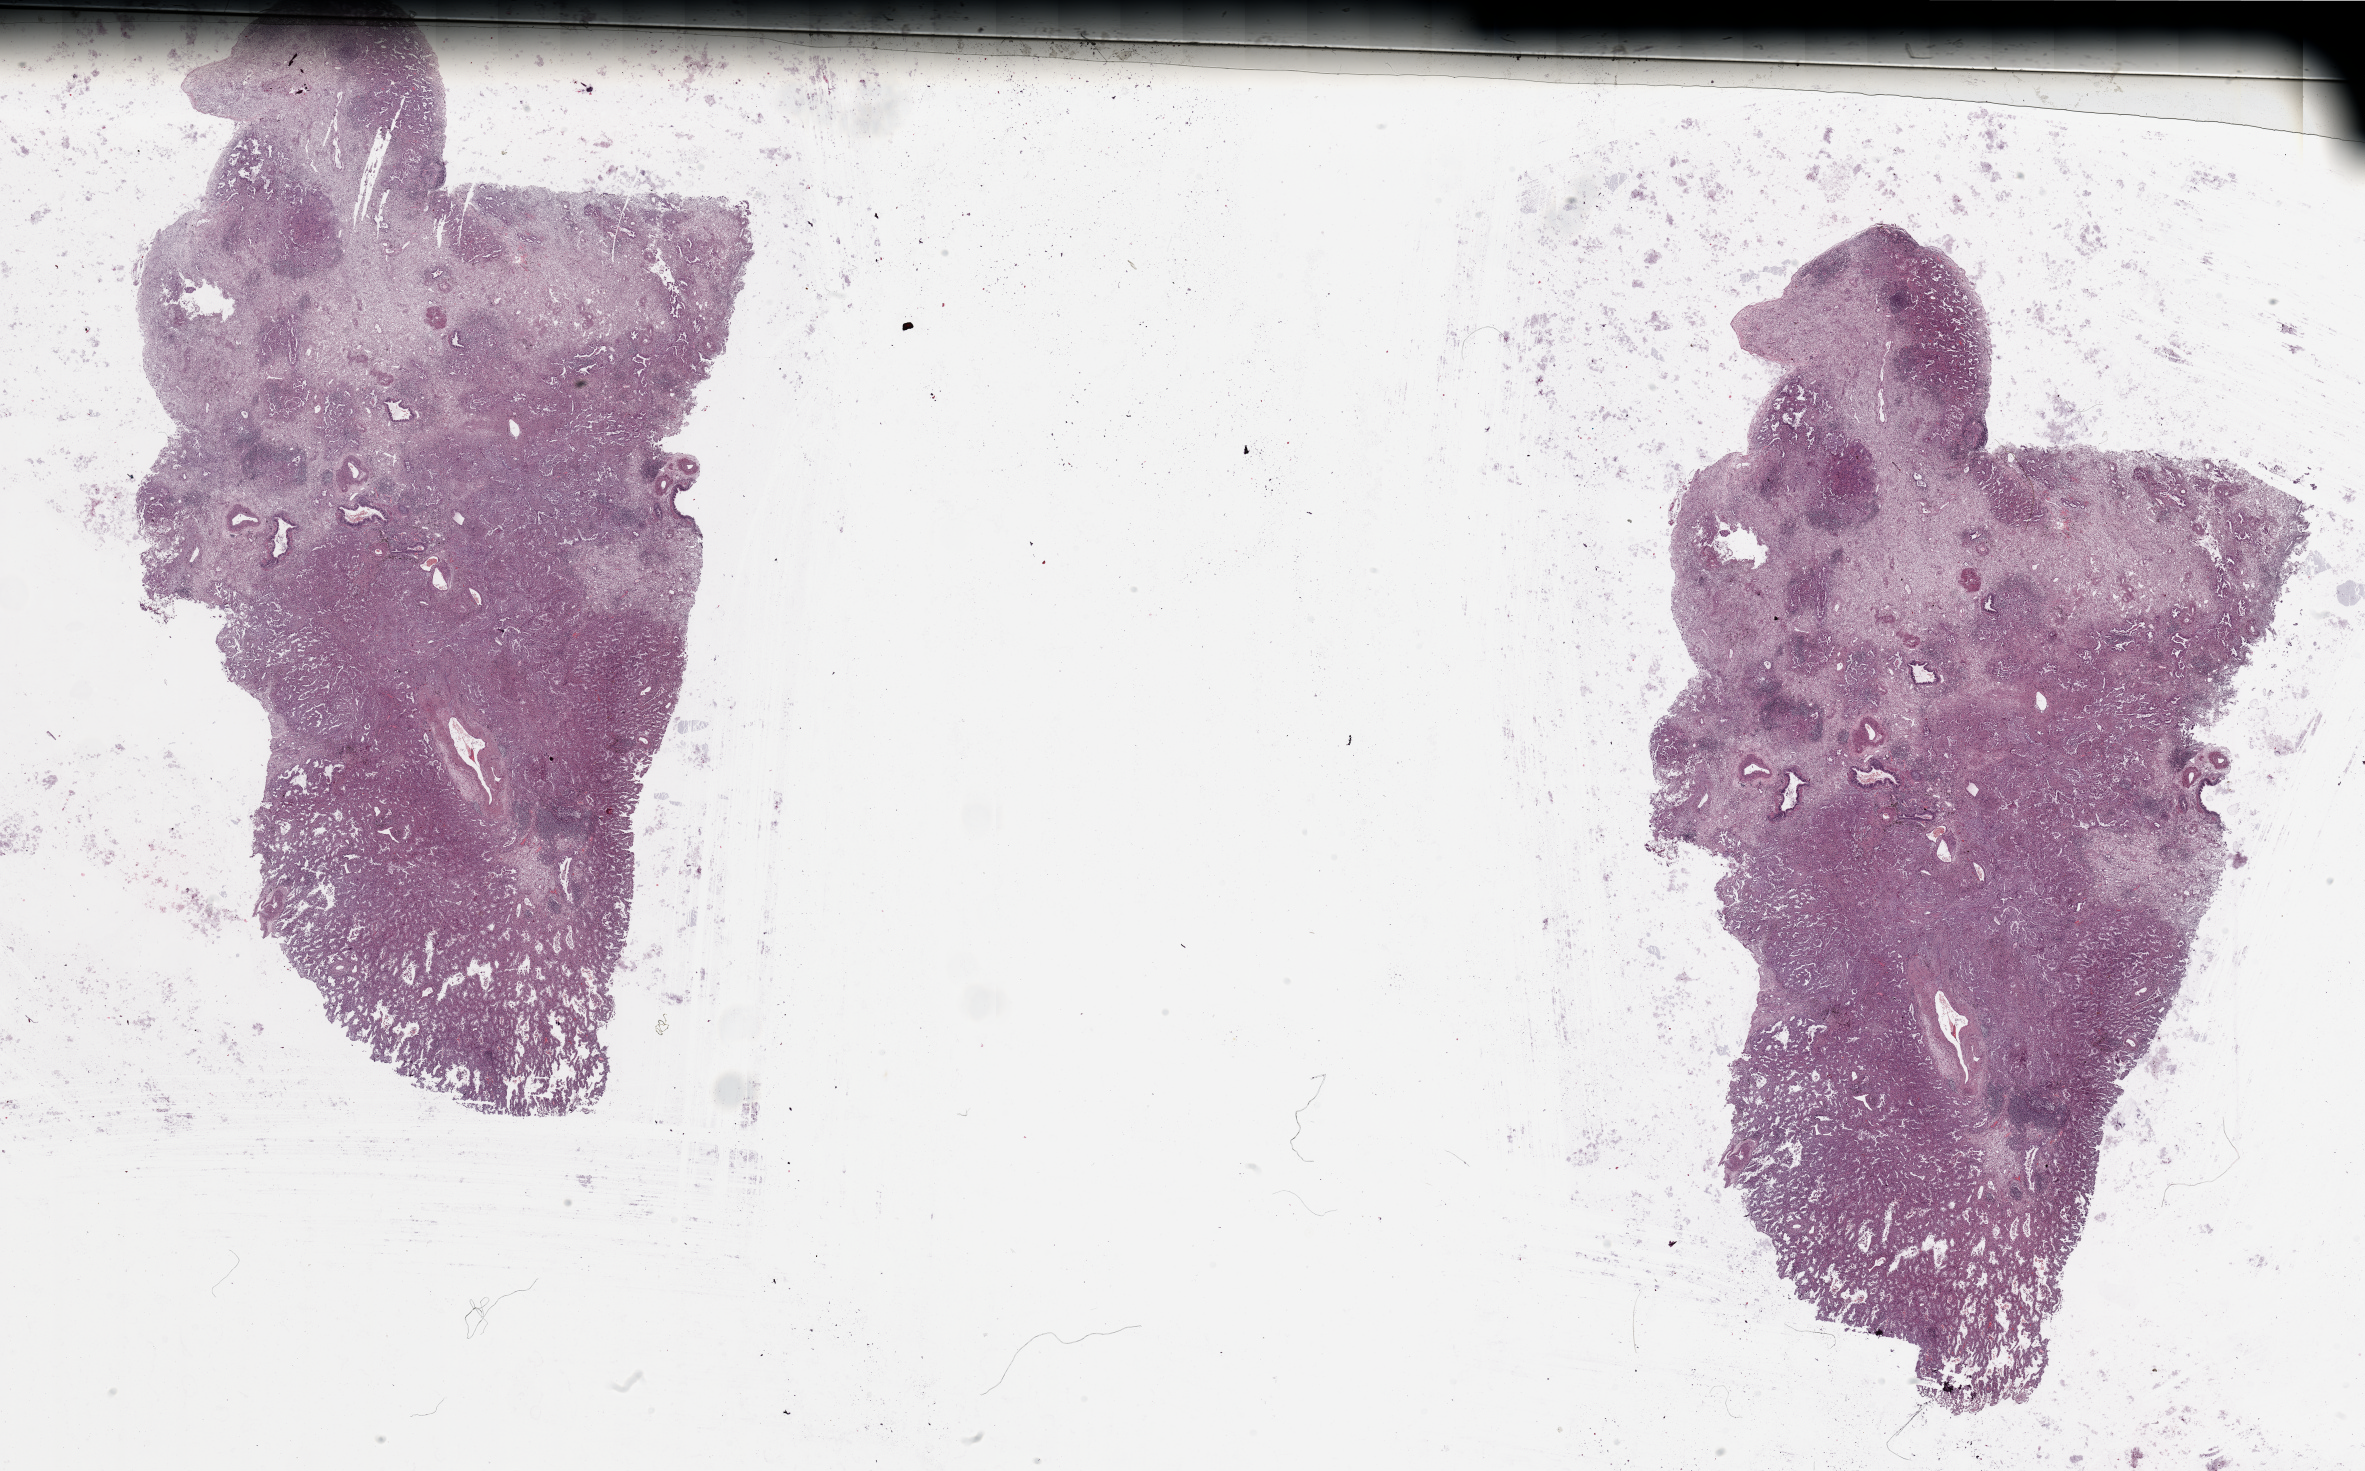
Digitized Hematoxylin and eosin (H&E) stained tissue section (whole slide), shown as a low-resolution overview of the whole scanned area (about 37.4 x 23.3 mm). Tumour tissue sample, lung. 61-year-old female patient. Histologic grade: G1 (well differentiated).
- histologic diagnosis: Adenocarcinoma, NOS
- primary tumour site (as recorded): right lower lobe
- AJCC pathologic stage: IA